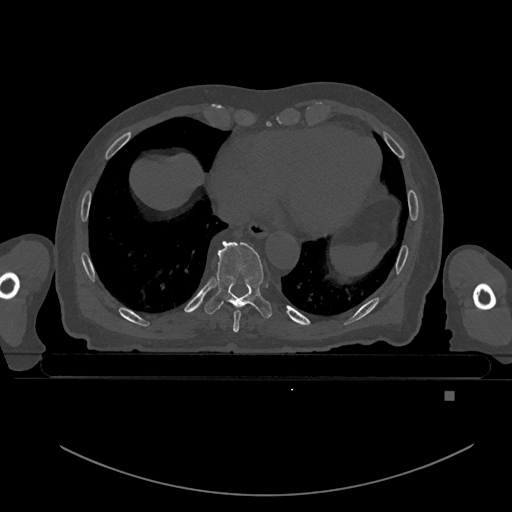
CT including the spine, one axial slice. Position 157 of 969 along the scan axis. Bone window (W 1800 / L 400 HU). 0.5 mm slice thickness. 512 × 512 image matrix, field of view 456 × 456 mm. Male patient, age 82 years. Case-level facts recorded for this patient, not image findings: primary cancer: prostate; vertebrae with lytic lesions (as recorded): T11, T9, T8, T2.
Annotated regions visible in this slice (semi-automatically segmented with operator editing):
- T8 vertebra: box from (x=233, y=310) to (x=241, y=333) px
- T9 vertebra: (x=205, y=241)–(x=272, y=319)